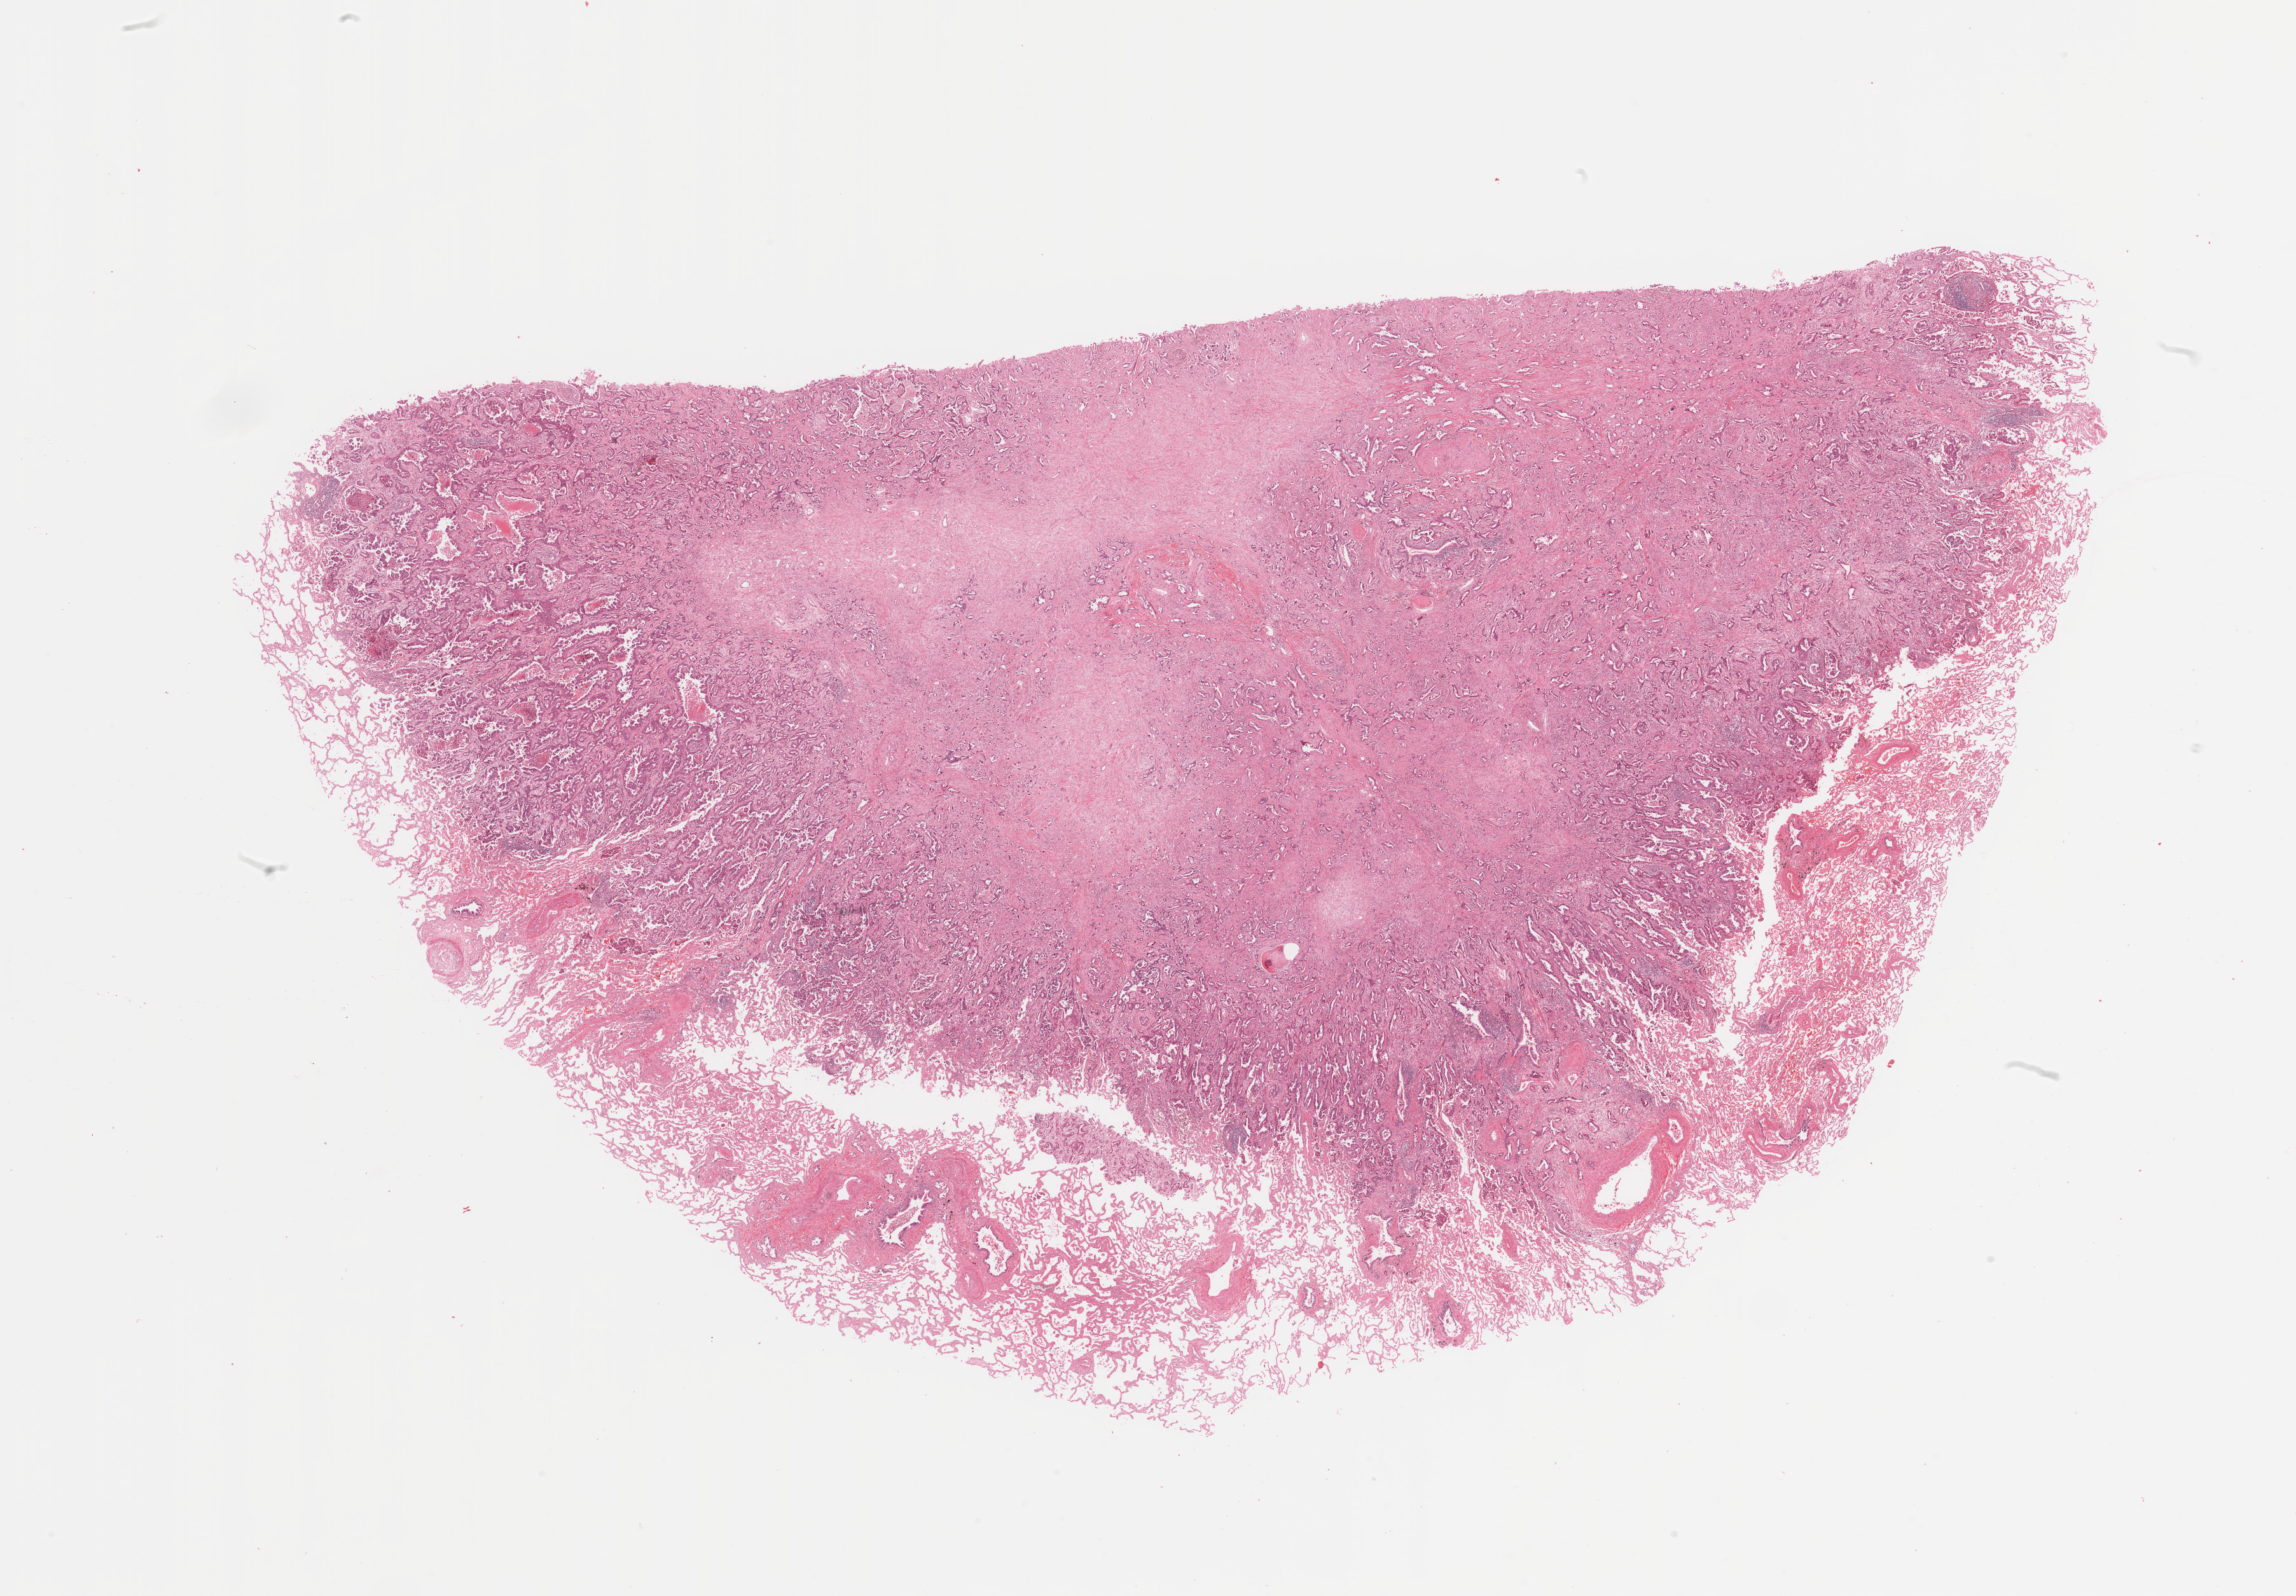
Whole-slide histology image, Hematoxylin and eosin (H&E) stained, whole scanned area (about 28.5 x 19.8 mm, from a 20x scan) shown as a low-resolution overview, tumour tissue sample, sampled site: lung. 65-year-old female patient. Composition of this section per pathologist review: tumour nuclei 70%, necrosis 0%.
Diagnosis: Adenocarcinoma, NOS.